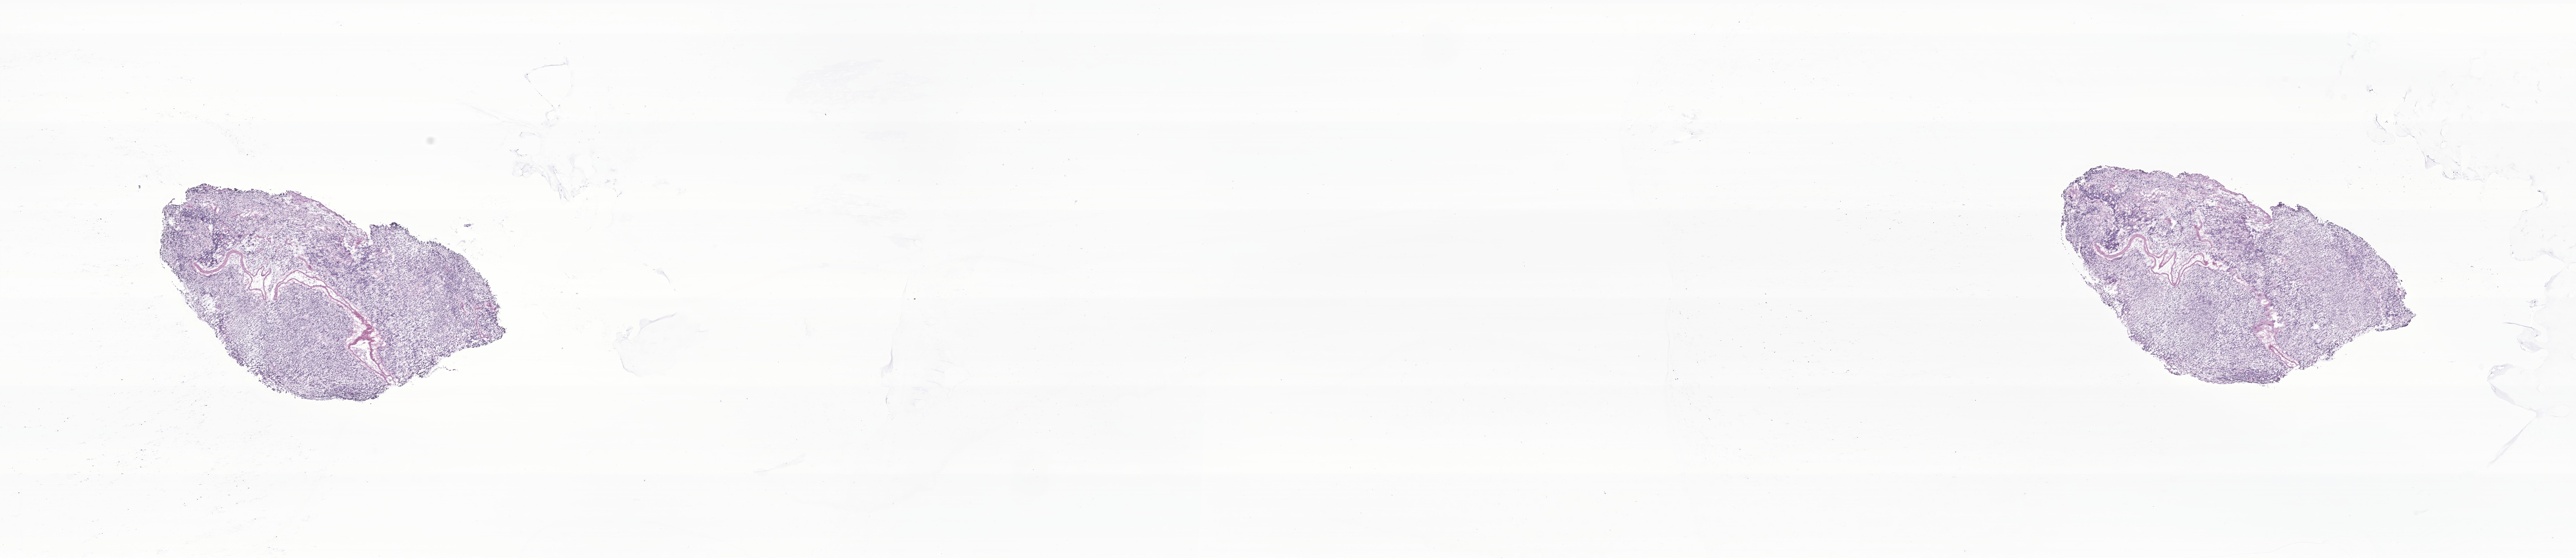
Whole-slide image, H&E stain of tumor tissue from the brain — shown as a low-resolution overview of the whole scanned area (about 31.2 x 6.8 mm). Frozen section (OCT-embedded). Male patient, age 212 months.
* recorded diagnosis: Neoplasm, malignant